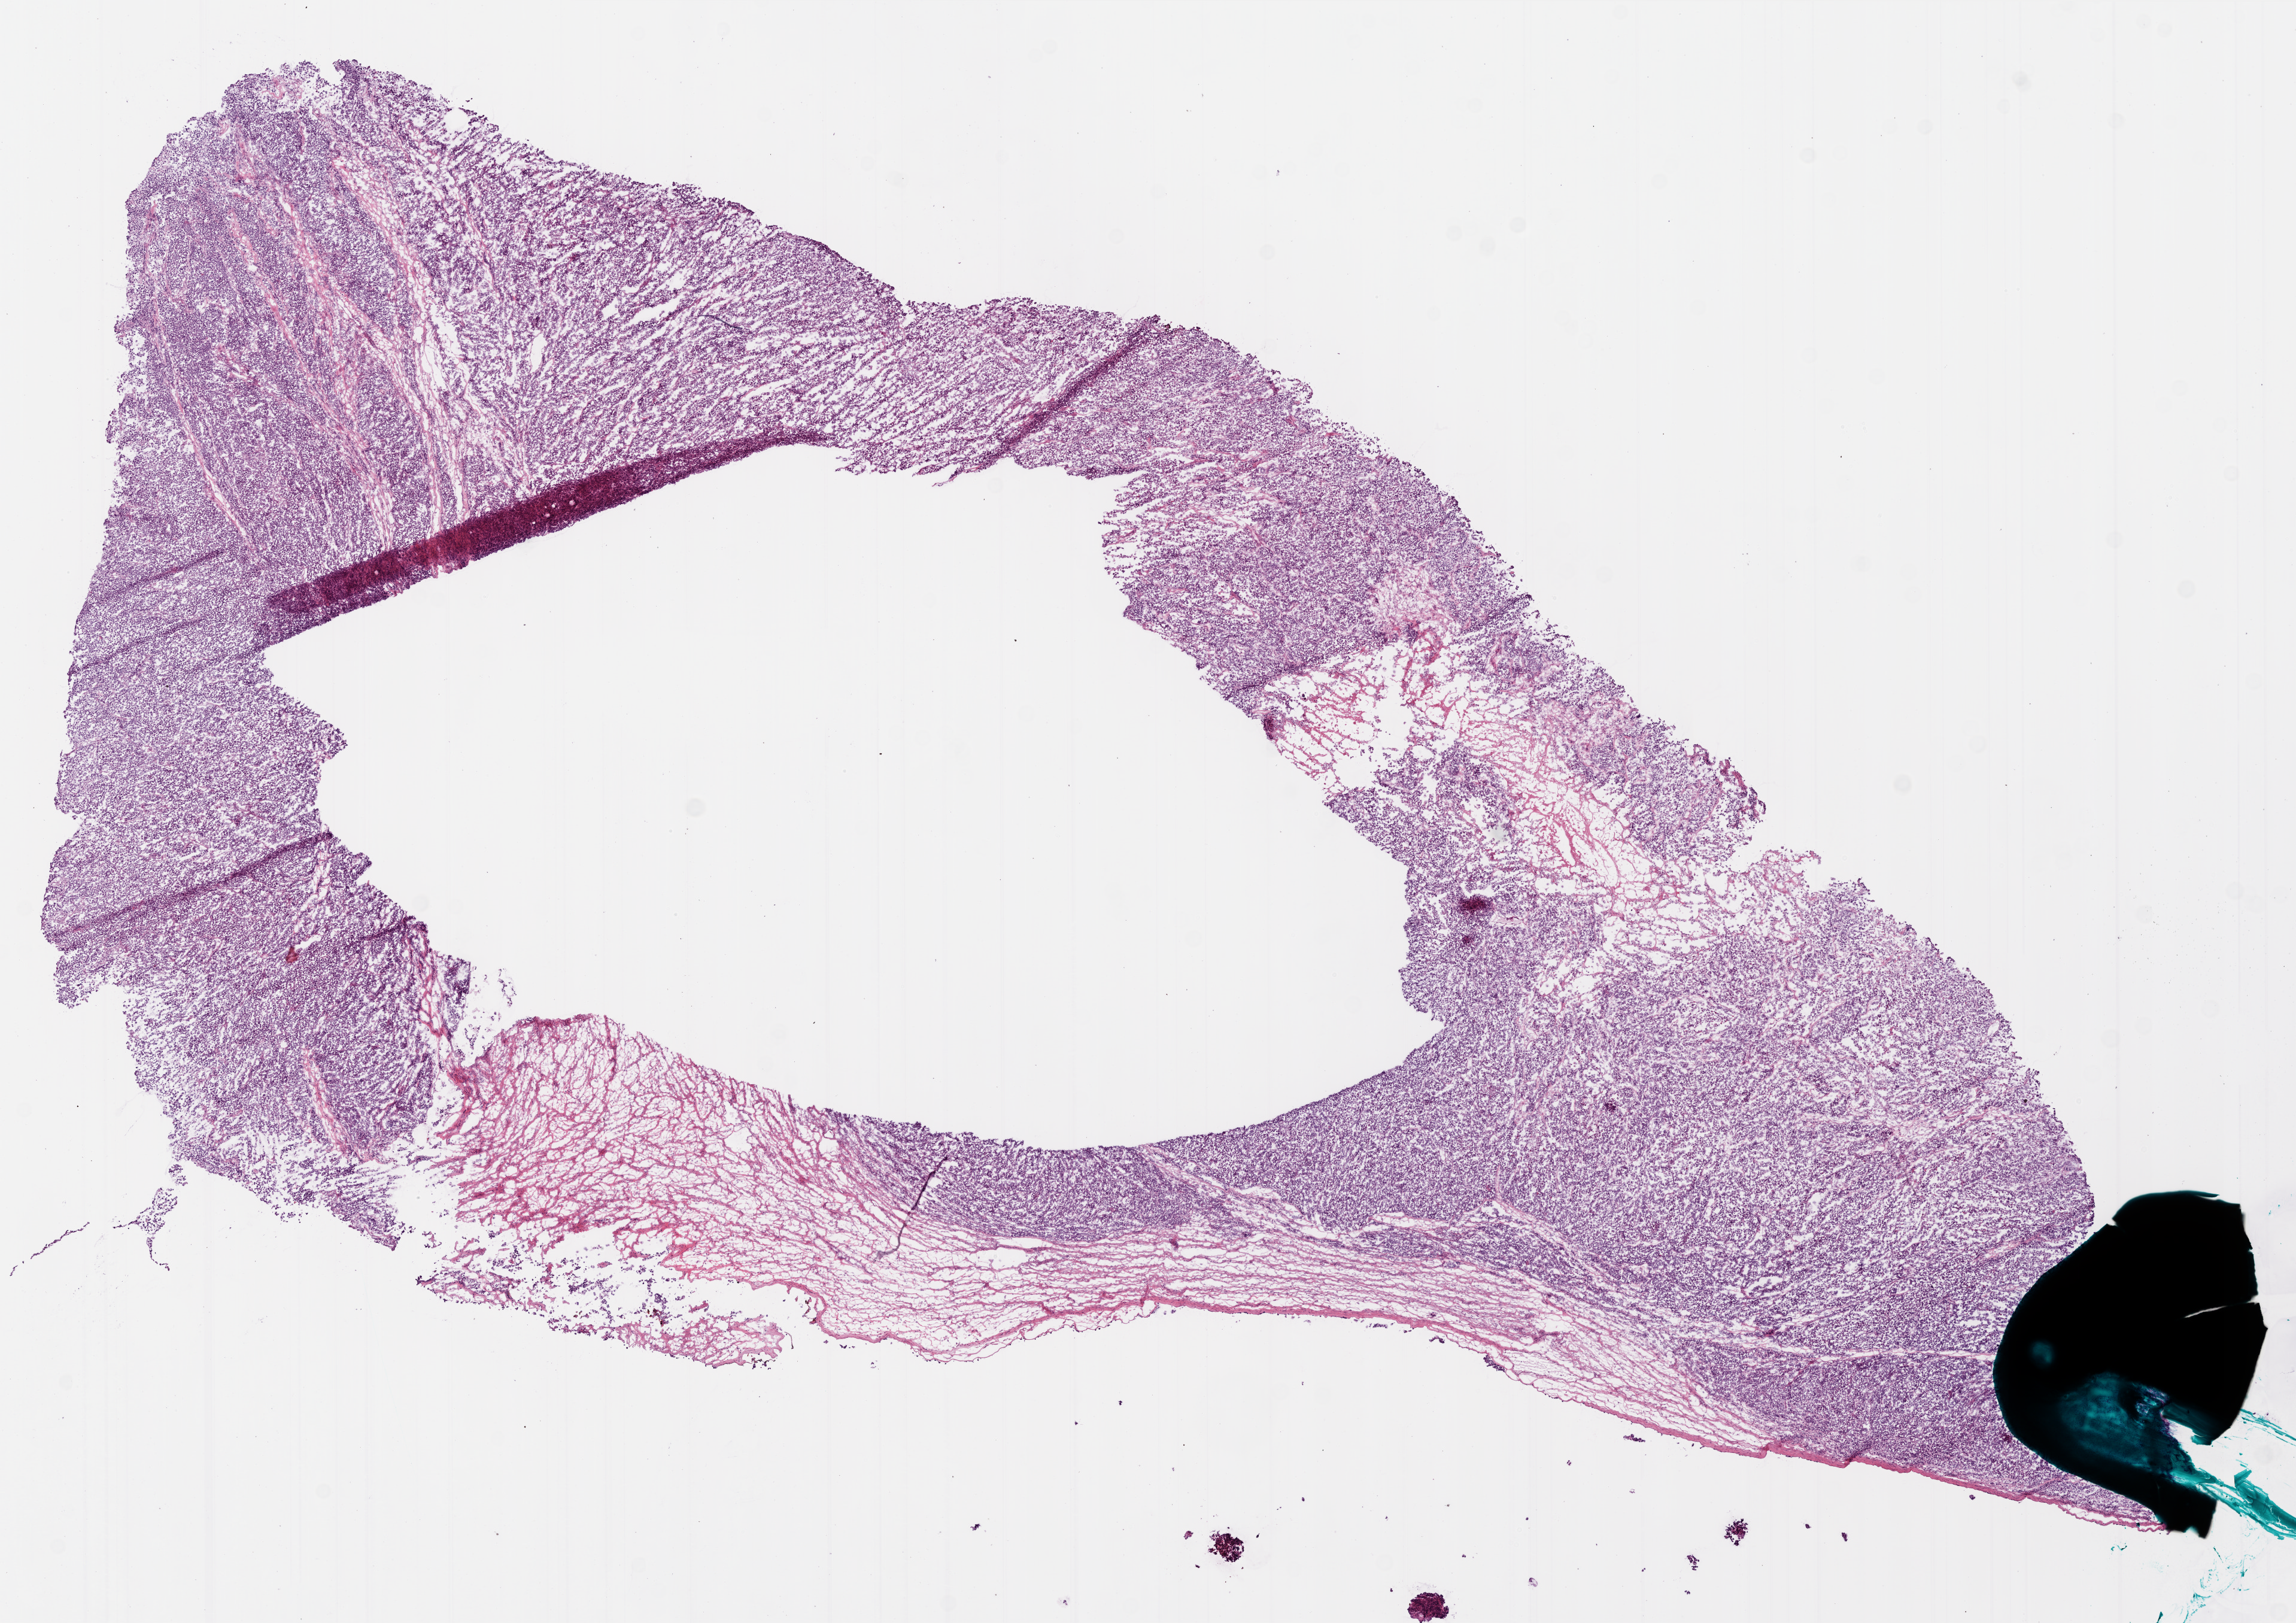
H&E whole-slide image — shown as a low-resolution overview of the whole scanned area (about 15.4 x 10.9 mm, slide scanned at 20x); frozen section from the bottom of the tissue portion; primary tumour sample from the ovary. Female patient; age at initial diagnosis 46 years. Histologic grade: G3 (poorly differentiated). Slide review estimates, as recorded: tumour cells 85%, tumour nuclei 90%, normal cells 0%, stromal cells 10%, necrosis 5%.
• diagnosis: Serous cystadenocarcinoma, NOS
• laterality: bilateral
• FIGO stage: IIIC